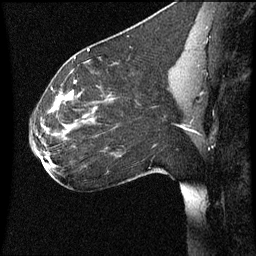
Breast MRI (dynamic contrast-enhanced), one sagittal slice; position 34 of 60 along the scan axis; dynamic contrast-enhanced series, image 2 of 3 at this slice position (ordered by acquisition); 1.5 T; TE 4.2 ms, TR 8.9 ms; 256 × 256 image matrix, field of view 200 × 200 mm. Patient: female, 35 years. Case-level facts recorded for this patient, not image findings: setting: breast cancer imaged before/during neoadjuvant chemotherapy; receptor status: HER2-positive.
Annotated regions visible in this slice (semi-automatic segmentation, software-assisted and operator-edited):
- analysis volume of interest (the breast-tissue region the enhancement analysis was run in; not a lesion): bounding box (x1, y1, x2, y2) in pixels: (28, 66, 177, 177)
- tumour enhancement mask (voxels above the 70 % enhancement threshold inside the analysis volume of interest): (58, 90, 111, 107)